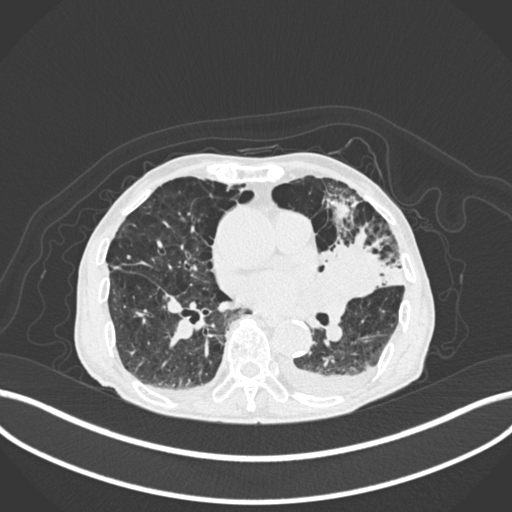
Chest CT, one axial slice. Slice 99 of 400 in the series (ordered by position). 120 kVp. Lung window (W 1500 / L -600 HU). 512 × 512 image matrix, field of view 400 × 400 mm. Male patient, age 90 years or older. Case-level facts recorded for this patient, not image findings: clinical TNM (as recorded): T2b N1 M0.
Outlined on this slice (rectangle marked by the reading radiologist):
- lung tumour (recorded histology: squamous cell carcinoma): bounding box (x1, y1, x2, y2) in pixels: (318, 235, 383, 302)